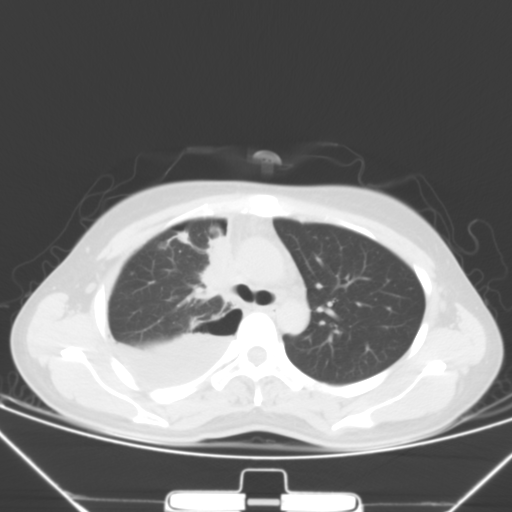
Chest CT, one axial slice; lung window (W 1500 / L -600 HU); 5 mm slice thickness; 512 × 512 image matrix. Patient: female, 28 years. From the clinical record (not read from this slice): clinical TNM (as recorded): T2 N0 M1a.
Annotated regions visible in this slice (rectangle marked by the reading radiologist):
- lung tumour (recorded histology: adenocarcinoma): bounding box [x1, y1, x2, y2] px = [193, 228, 234, 307]